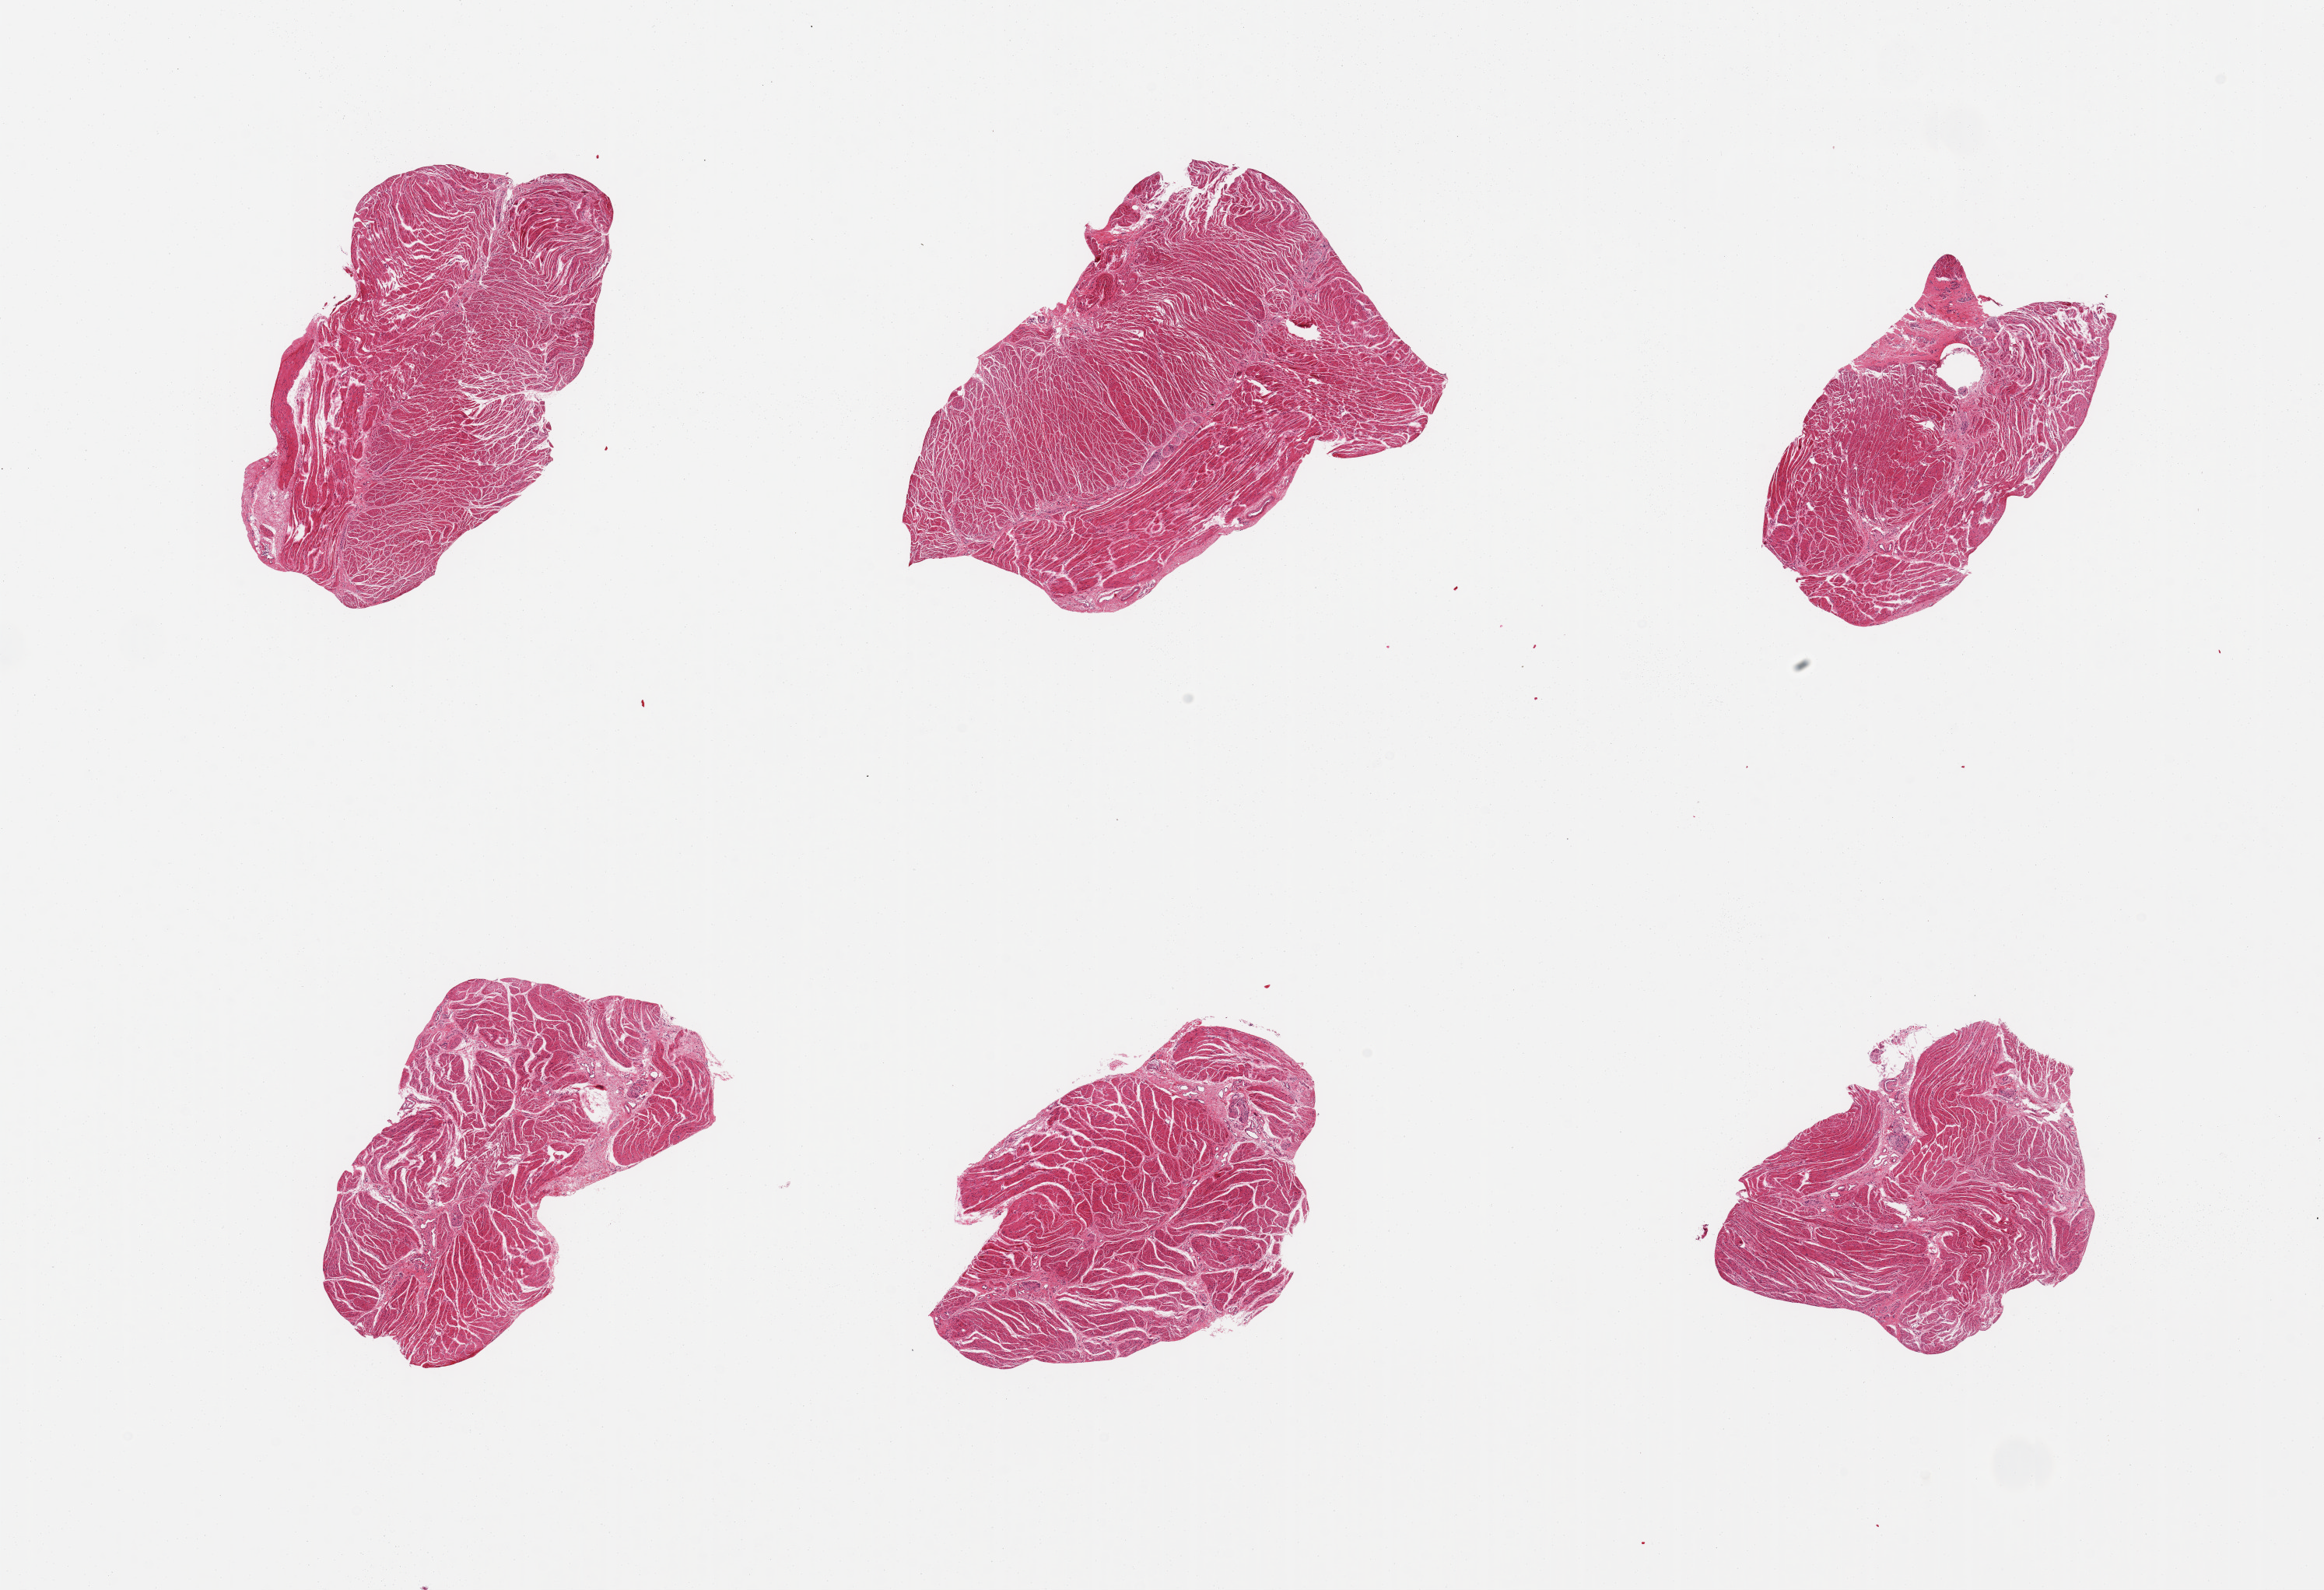
Haematoxylin and eosin whole-slide image, brightfield, shown as a low-resolution overview of the whole scanned area (about 23.6 x 16.2 mm, slide scanned at 20x). PAXgene-fixed paraffin-embedded (PFPE) section. Section of esophageal muscle (target tissue). Donor tissue sample. Female donor.
• reviewer comment on this tissue sample: 6 pieces; target muscularis